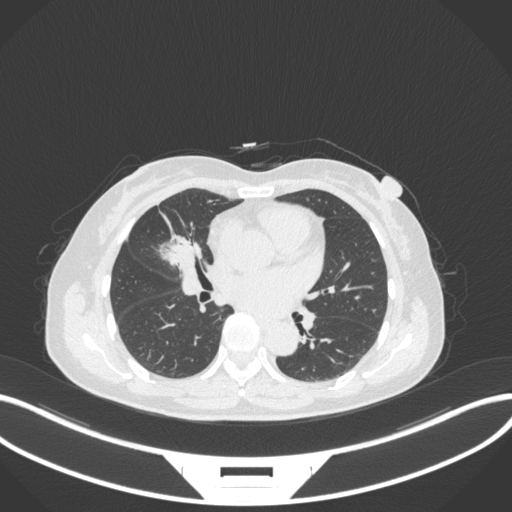
Chest CT, one axial slice; position 152 of 282 along the scan axis; reconstruction kernel B31f; 120 kVp; lung window (W 1500 / L -600 HU); 1 mm slice thickness; 512 × 512 image matrix, field of view 400 × 400 mm. Female patient, age 51 years. From the clinical record (not read from this slice): clinical TNM (as recorded): T1c N0 M0.
Annotated regions visible in this slice (rectangle marked by the reading radiologist):
- lung tumour (recorded histology: adenocarcinoma): box from (x=150, y=224) to (x=200, y=272) px